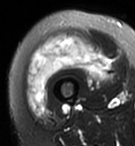
MRI of an extremity soft-tissue mass, one axial slice; position 29 of 95 along the scan axis; T2-weighted fat-saturated; MR volume resampled by the dataset authors to the PET/CT grid (not the native acquisition matrix); 135 × 146 image matrix. Female patient. Case-level facts recorded for this patient, not image findings: histological type: pleiomorphic undifferentiated sarcoma; grade: high; site of the primary tumour: right quadricep.
Annotated regions visible in this slice (expert contour drawn on MRI and transferred to this co-registered scan by the dataset authors):
- gross tumour volume including surrounding oedema: bounding box (x1, y1, x2, y2) in pixels: (26, 36, 109, 115)
- gross tumour volume (mass): (26, 36, 109, 115)